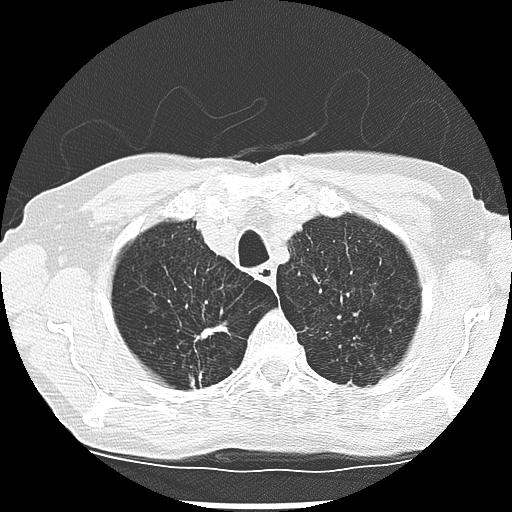
Low-dose screening chest CT, one axial slice. Position 230 of 265 along the scan axis. Lung window (W 1500 / L -600 HU). 512 × 512 image matrix.
Structures marked on this image (outlined manually by an expert reader):
- lesion 2 (tumor, upper lobe of right lung): box from (x=197, y=326) to (x=217, y=340) px